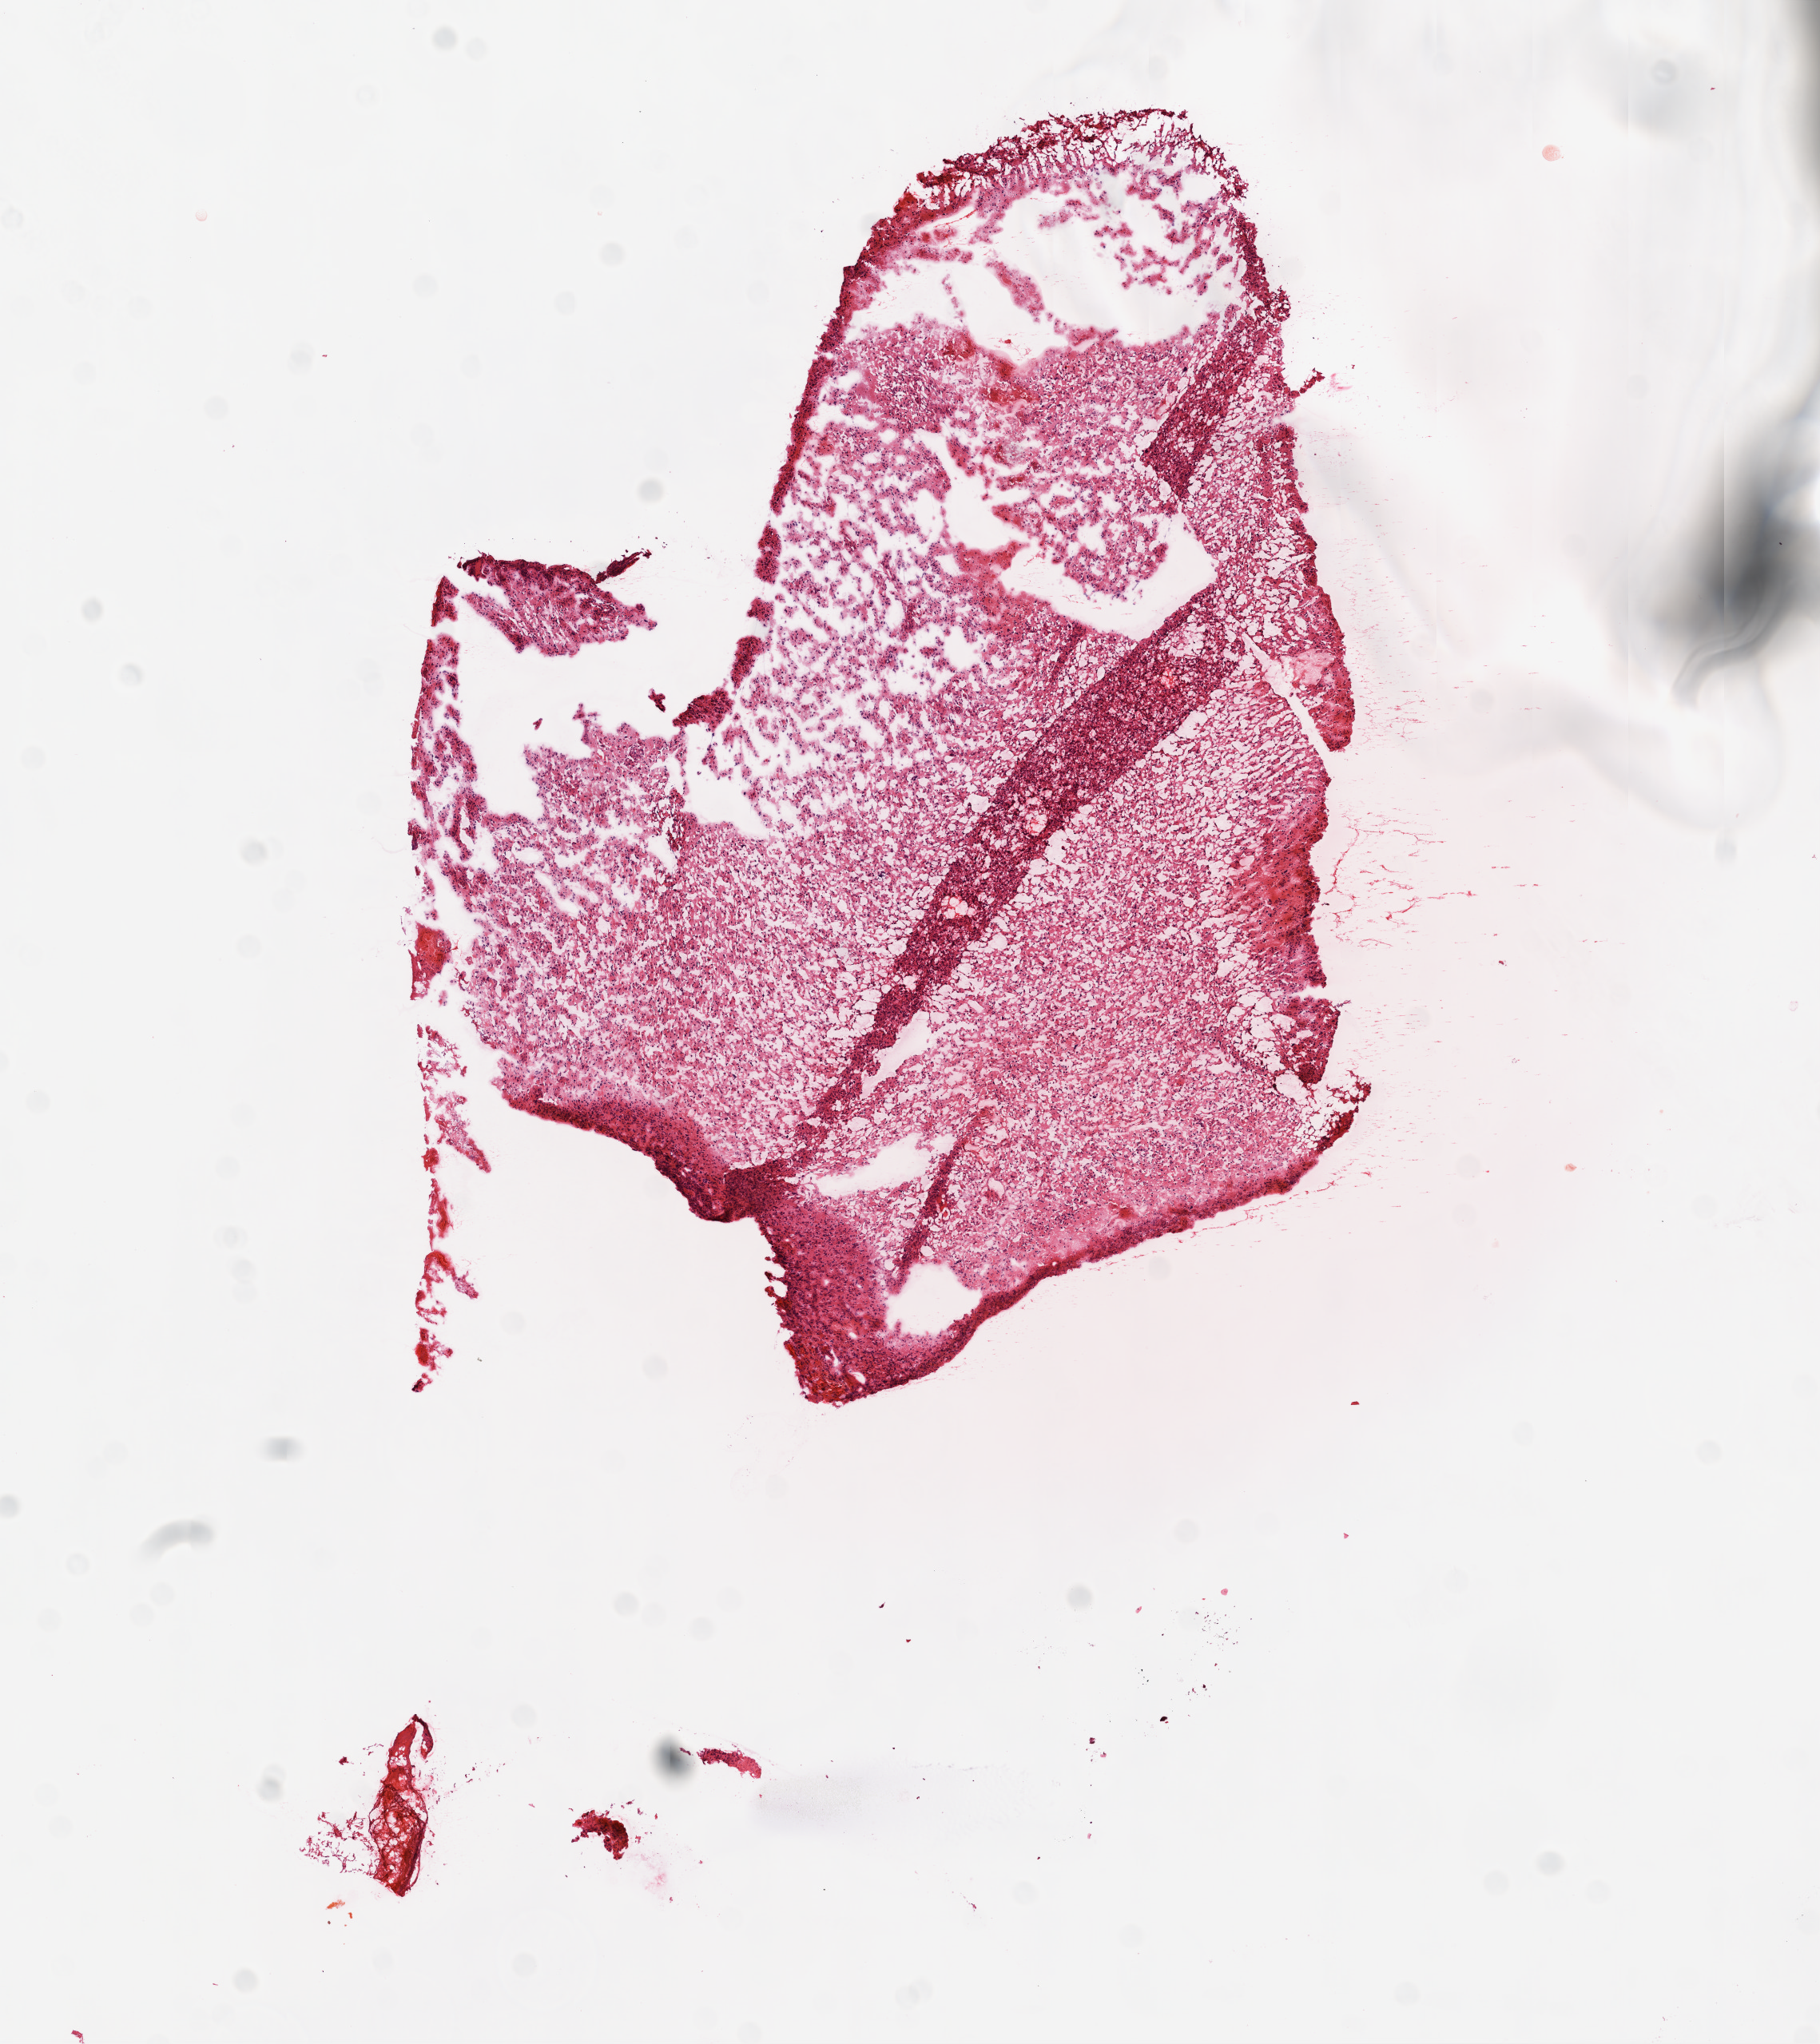
Hematoxylin and eosin (H&E) stained whole-slide image, low-resolution overview of the scanned area, about 9.2 x 10.3 mm (from a 20x scan); frozen section from the top of the tissue portion; brain, primary tumour sample. Female patient; age at initial diagnosis 53 years. Pathologist review of this section (percent, as recorded): tumour cells 85%, tumour nuclei 85%, normal cells 15%, stromal cells 5%, necrosis 0%.
Pathologic diagnosis: Glioblastoma.